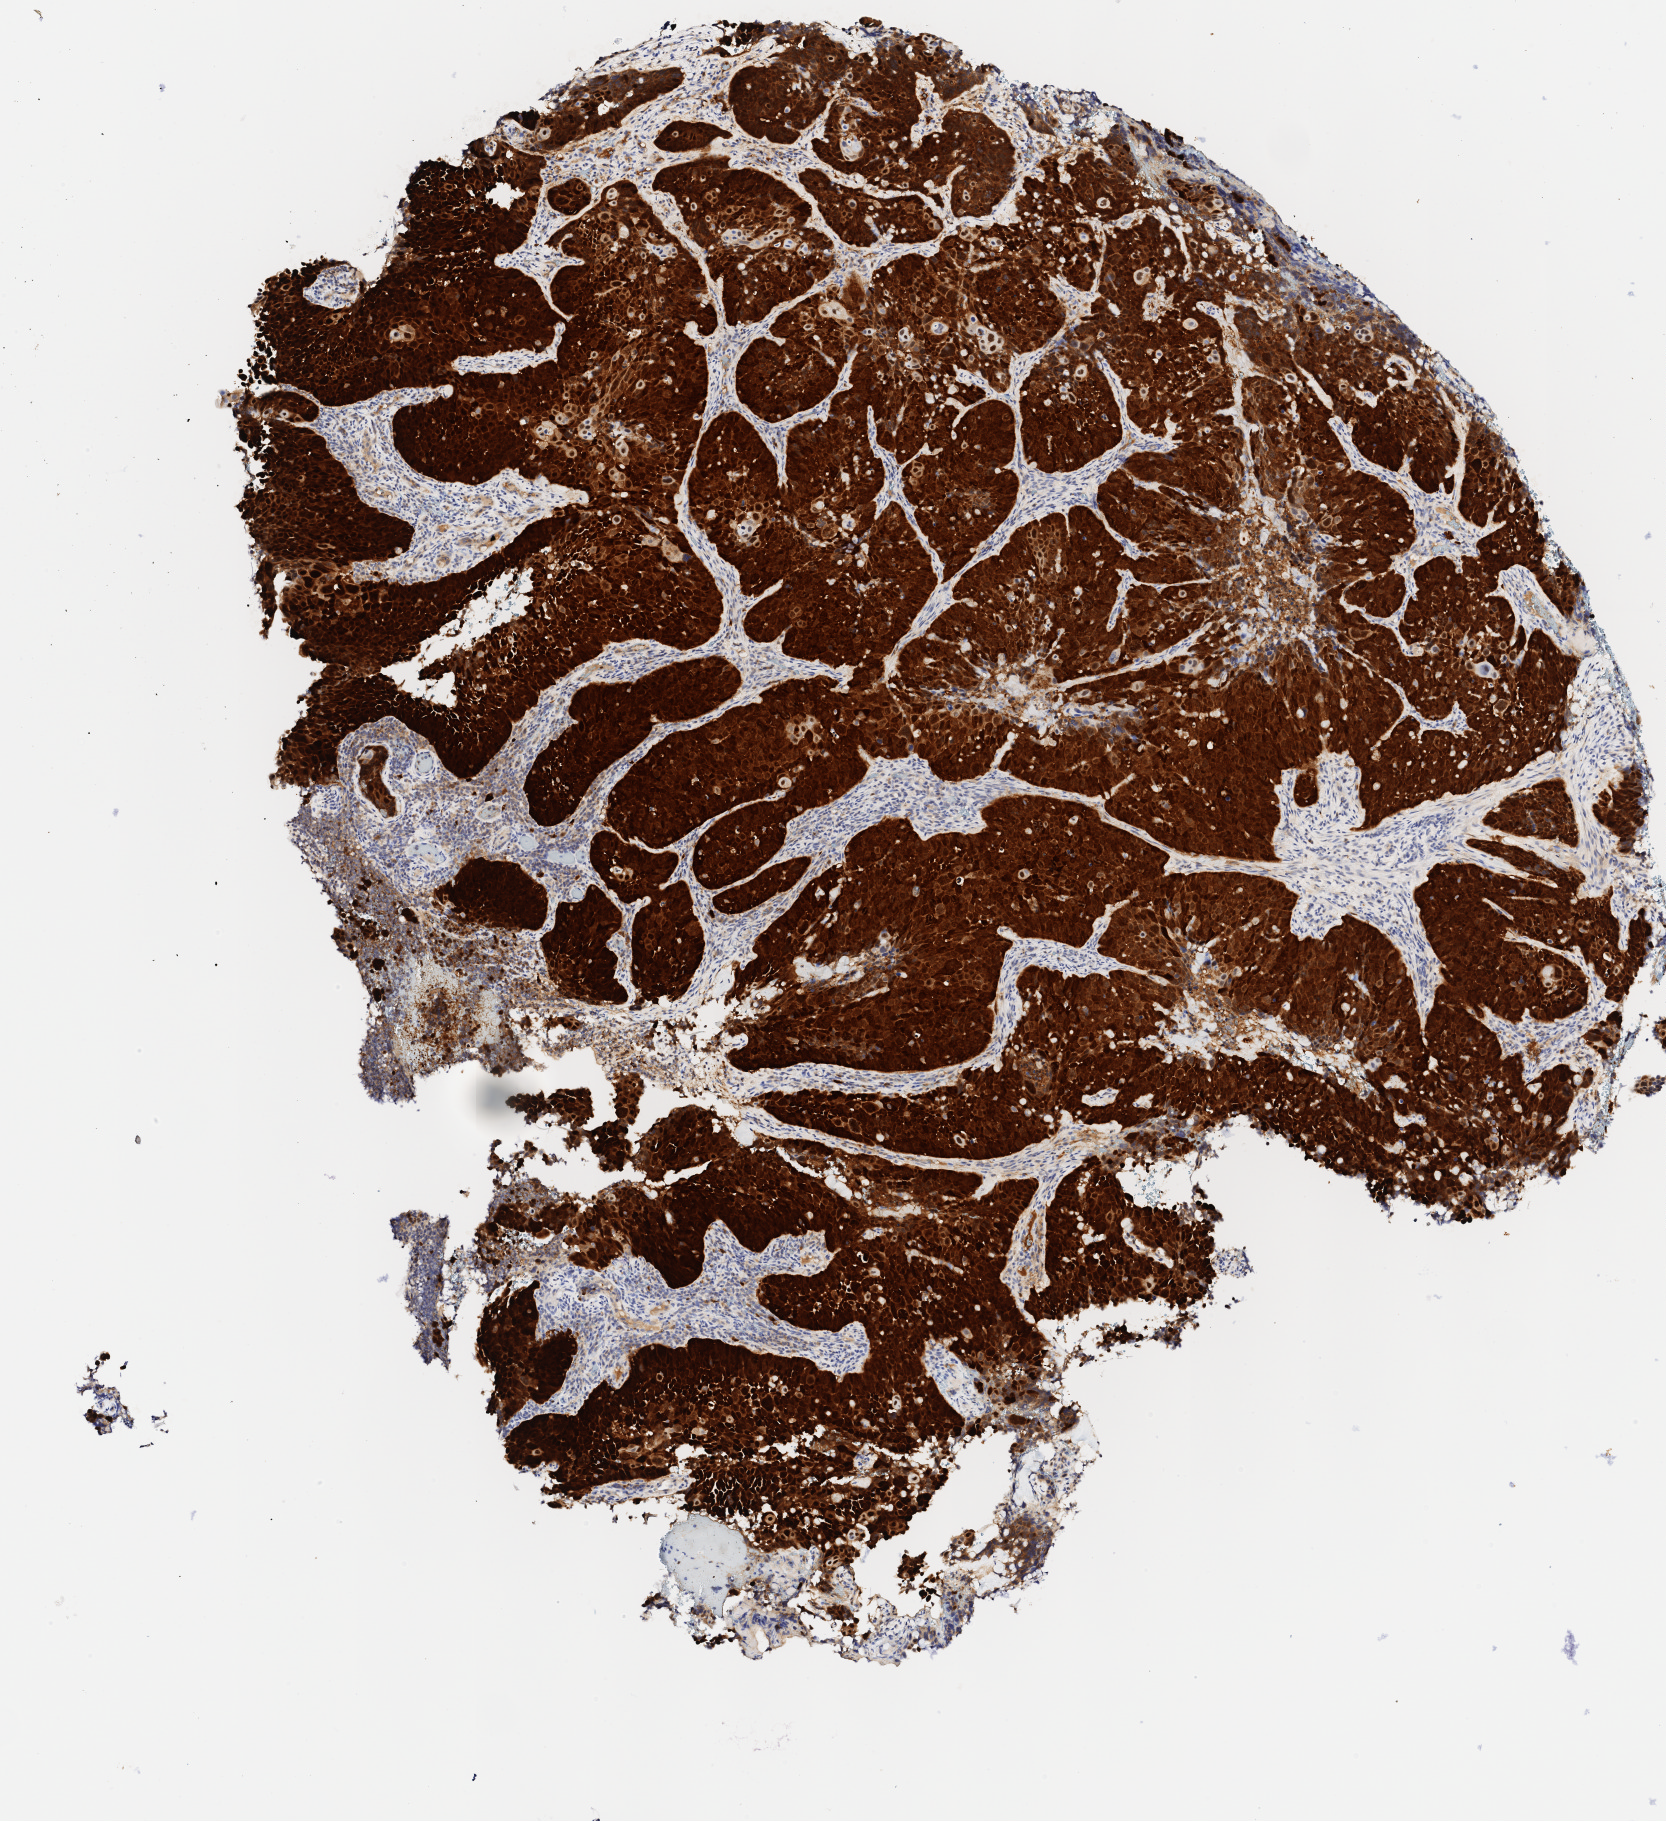
Immunohistochemistry (IHC) whole-slide image stained for p16 (p16INK4a) — whole scanned area (about 3.3 x 3.6 mm) shown as a low-resolution overview, specimen: tumor tissue, anatomic site: cervix. Patient female; aged 58.
Diagnosis: Squamous cell carcinoma, large cell, nonkeratinizing, NOS.